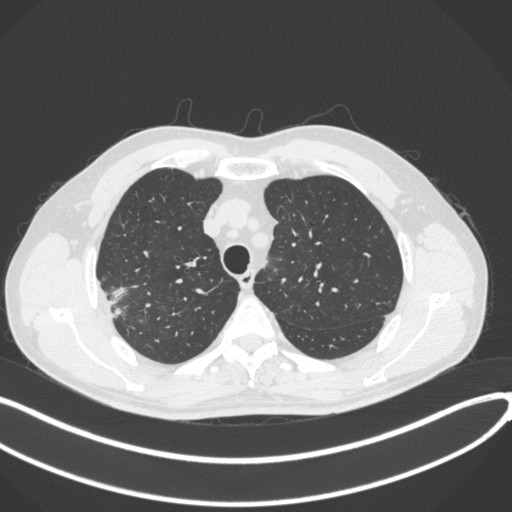
Chest CT, one axial slice. Slice 331 of 381 in the series (ordered by position). 120 kVp. Lung window (W 1500 / L -600 HU). 1 mm slice thickness. 512 × 512 image matrix. Patient: male, 62 years. From the clinical record (not read from this slice): clinical TNM (as recorded): T1c N0 M0; histopathological grade: G2-3.
Outlined on this slice (bounding box drawn by a radiologist):
- lung tumour (recorded histology: adenocarcinoma): bounding box [x1, y1, x2, y2] px = [104, 282, 131, 318]